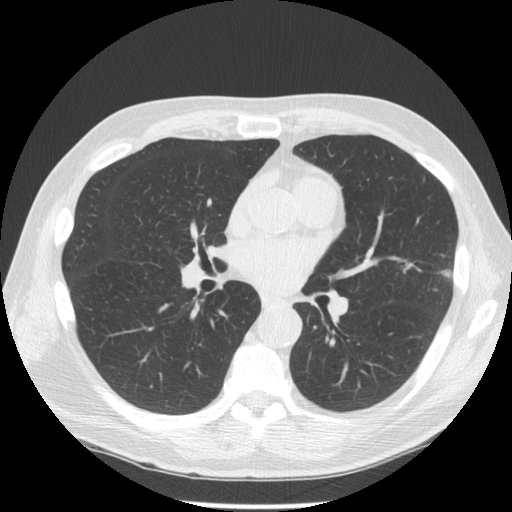
Low-dose screening chest CT, one axial slice. Slice 73 of 134 in the series (ordered by position). Reconstruction kernel STANDARD. 120 kVp. Lung window (W 1500 / L -600 HU). 512 × 512 image matrix, field of view 350 × 350 mm.
Outlined on this slice (manually delineated by an expert):
- lesion 1 (tumor, upper lobe of left lung): bounding box <442,270,451,277> (left, top, right, bottom; pixels)